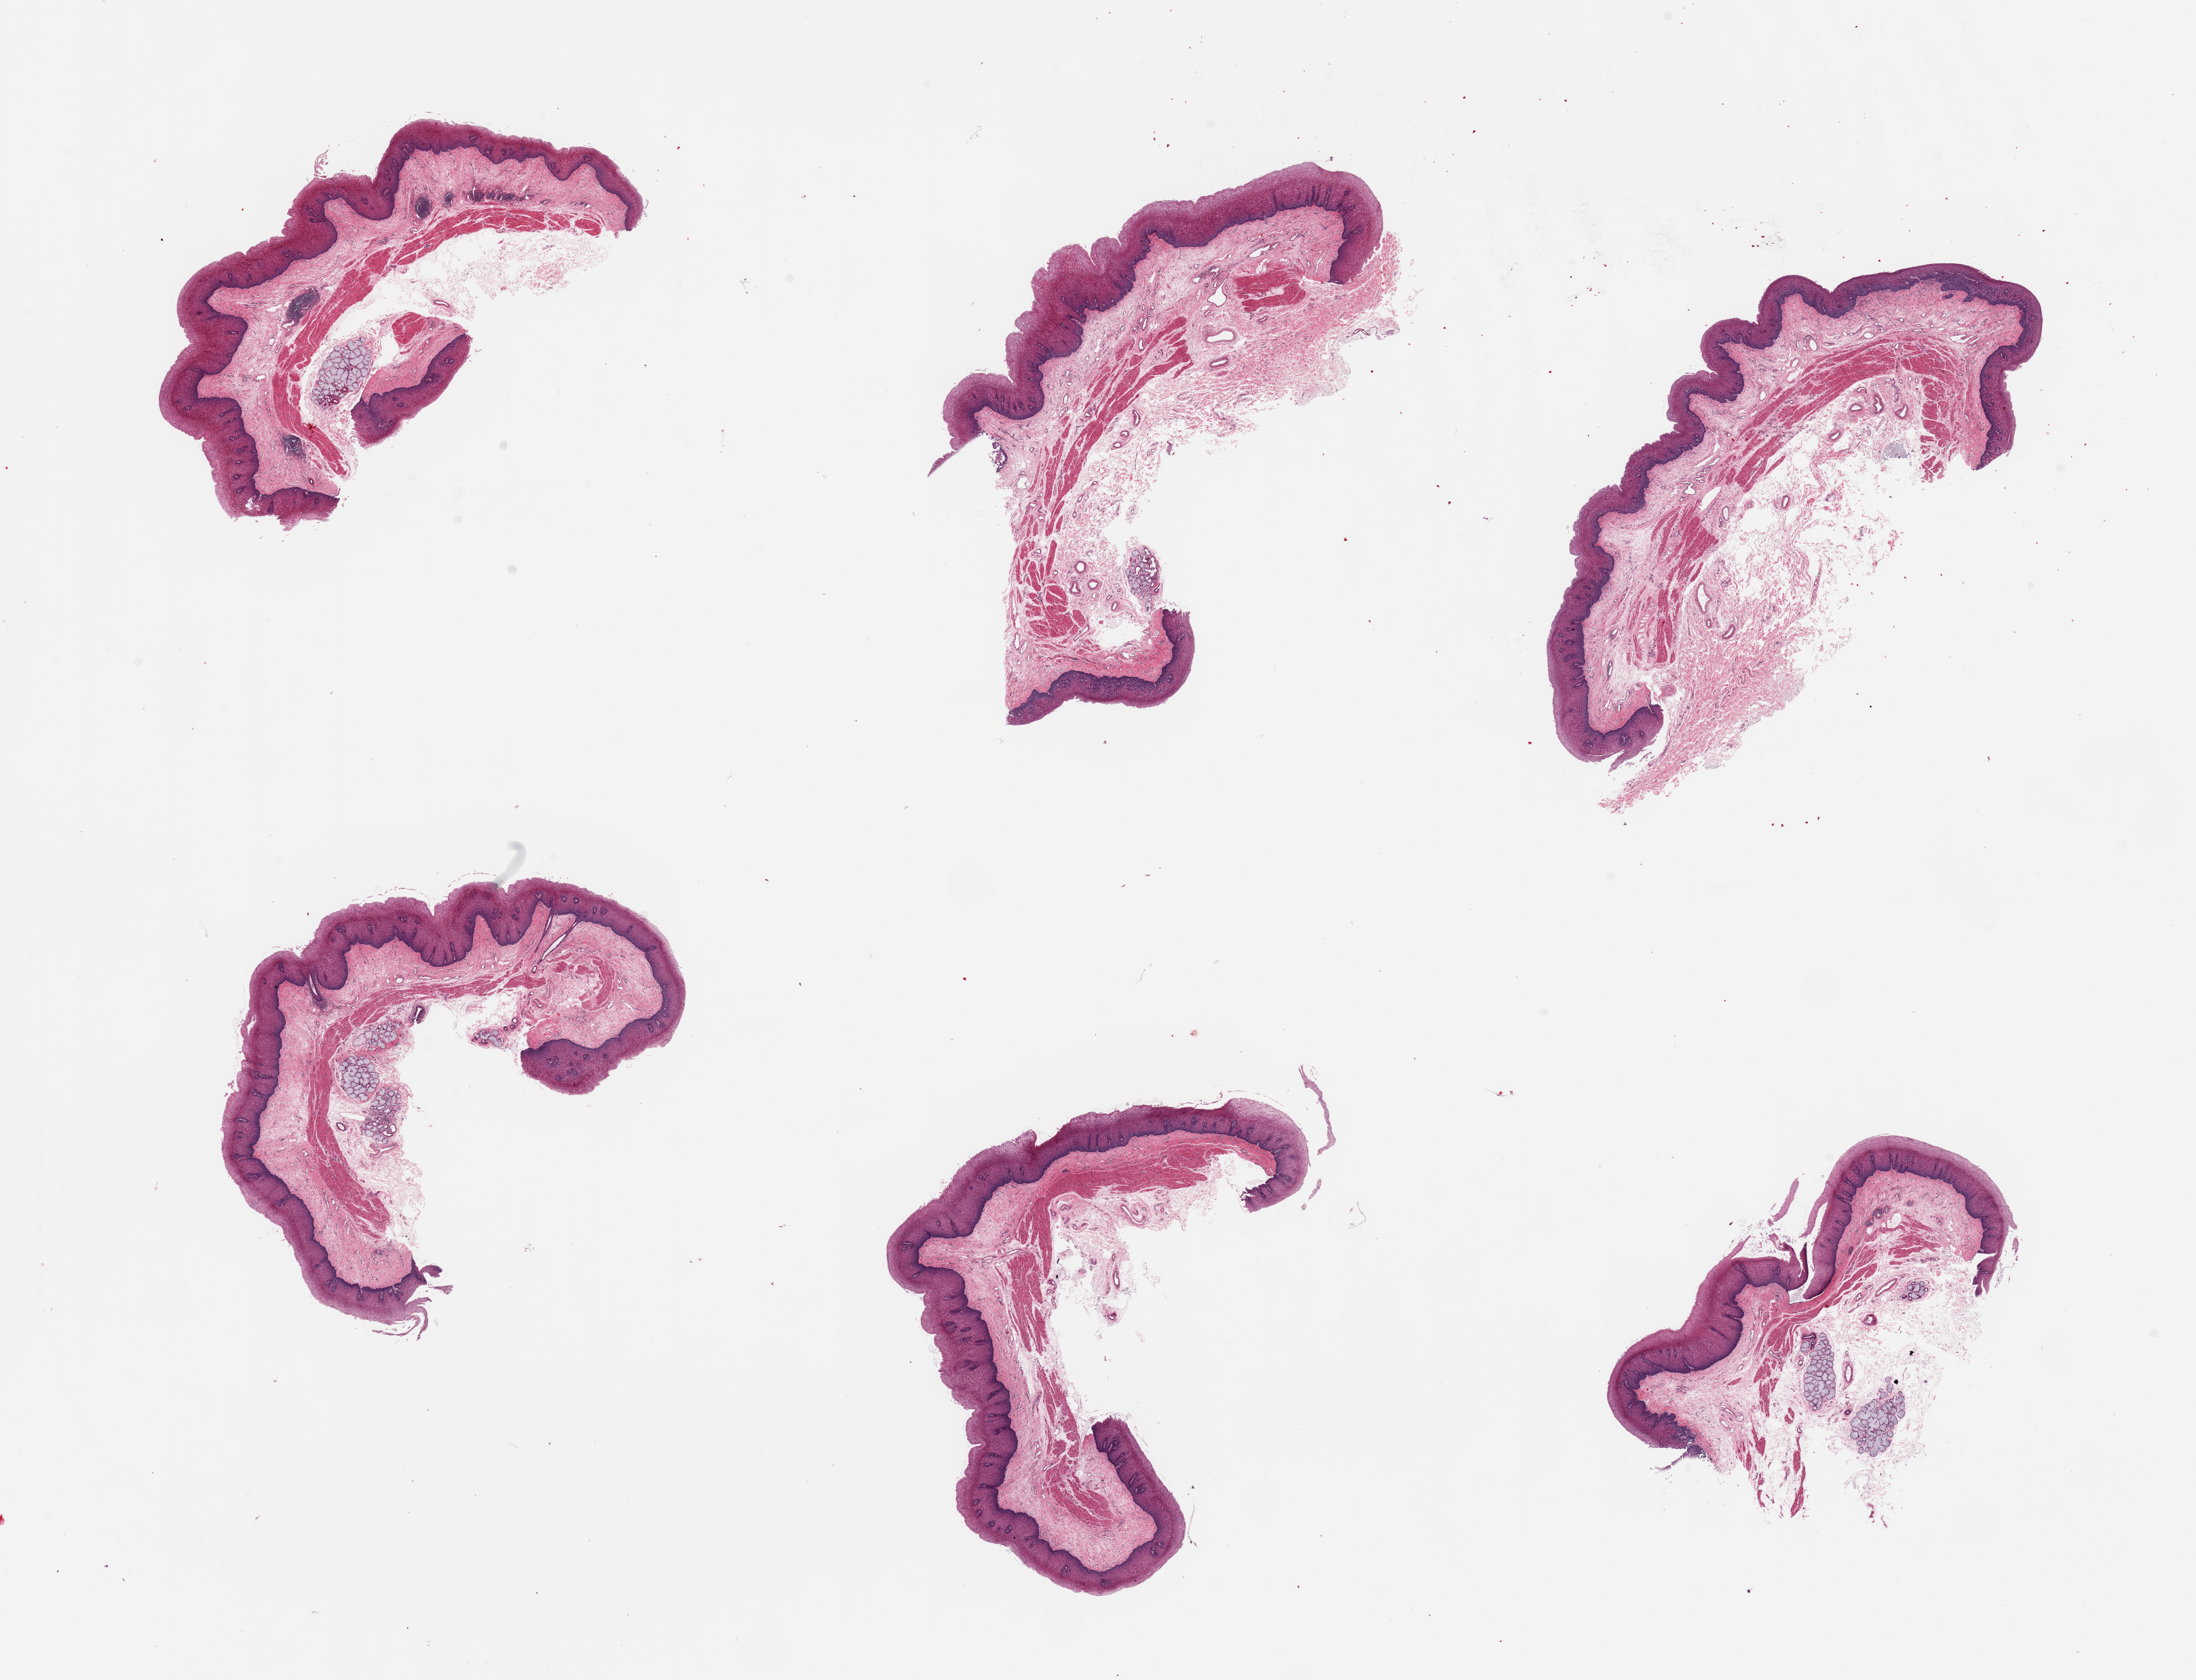
Whole-slide image, H&E stain, low-resolution overview of the scanned area, about 25.6 x 19.6 mm, PAXgene-fixed paraffin-embedded (PFPE) section, sampled site (target tissue): esophageal mucous membrane, donor tissue sample. Donor sex: female.
Reviewer comment on this tissue sample: 6 pieces.